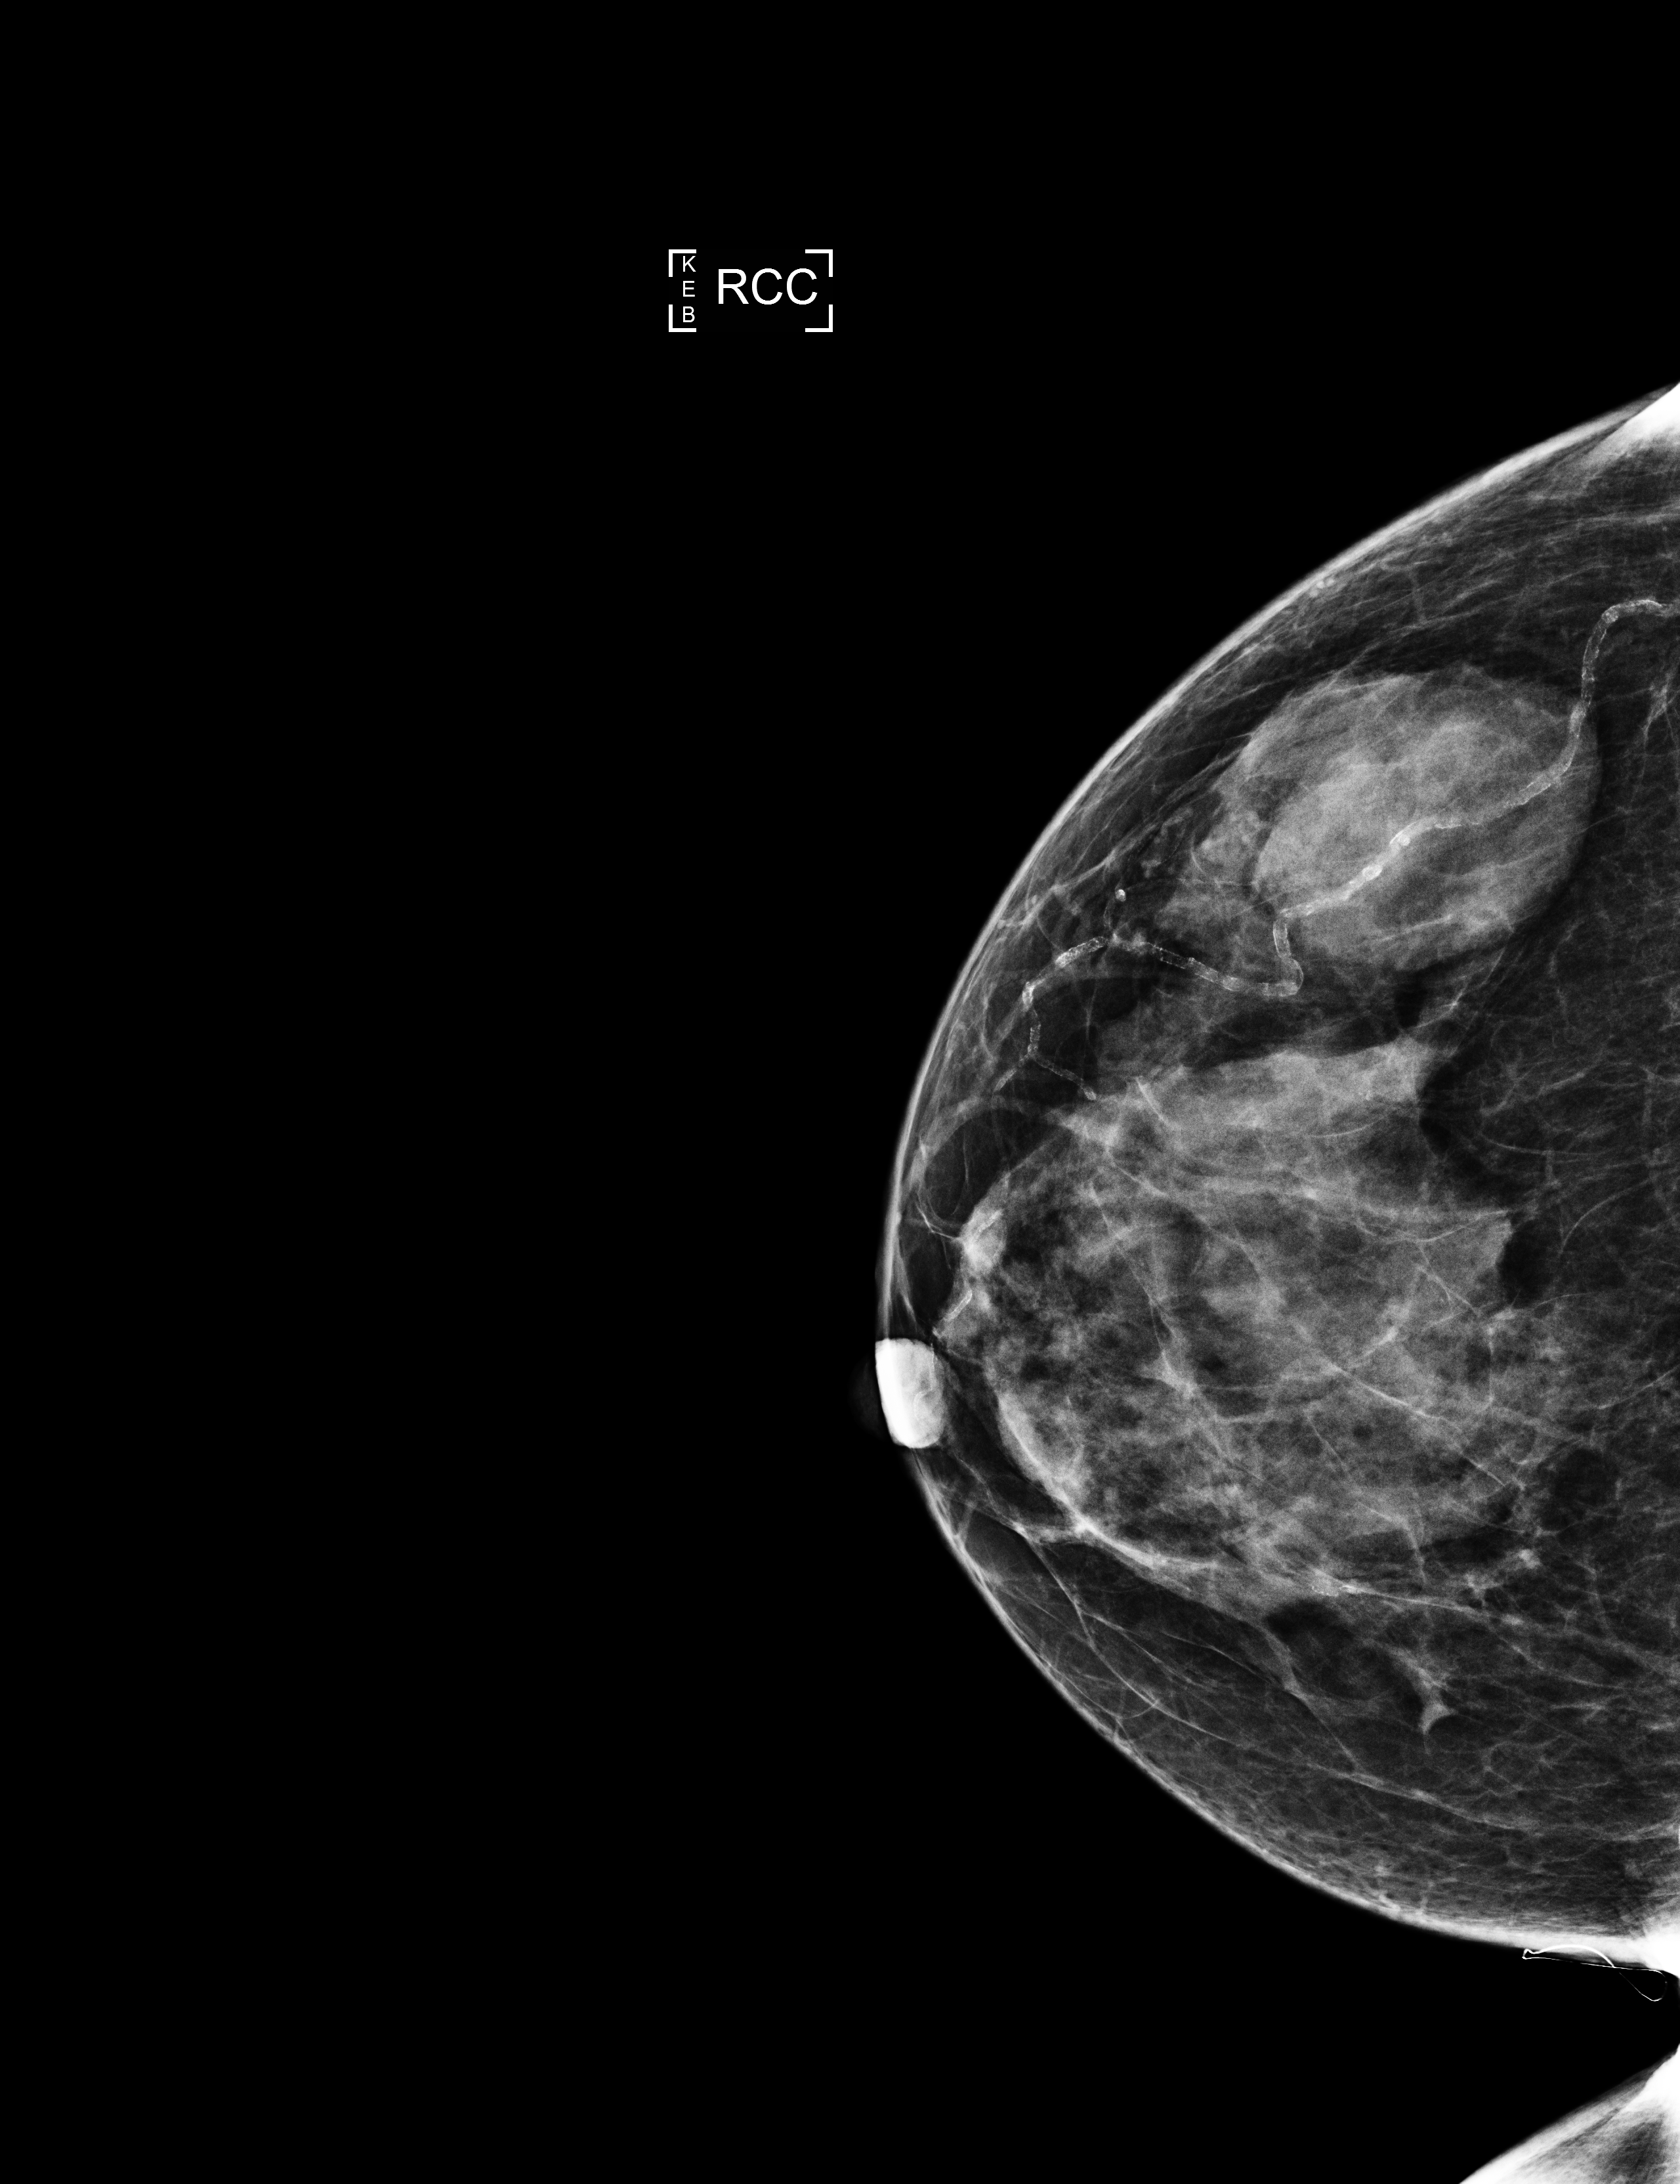
Screening examination; compressed breast thickness 38 mm. Patient: female, 76 years.
Image type: full-field digital mammogram. Breast: right. Projection: CC view.